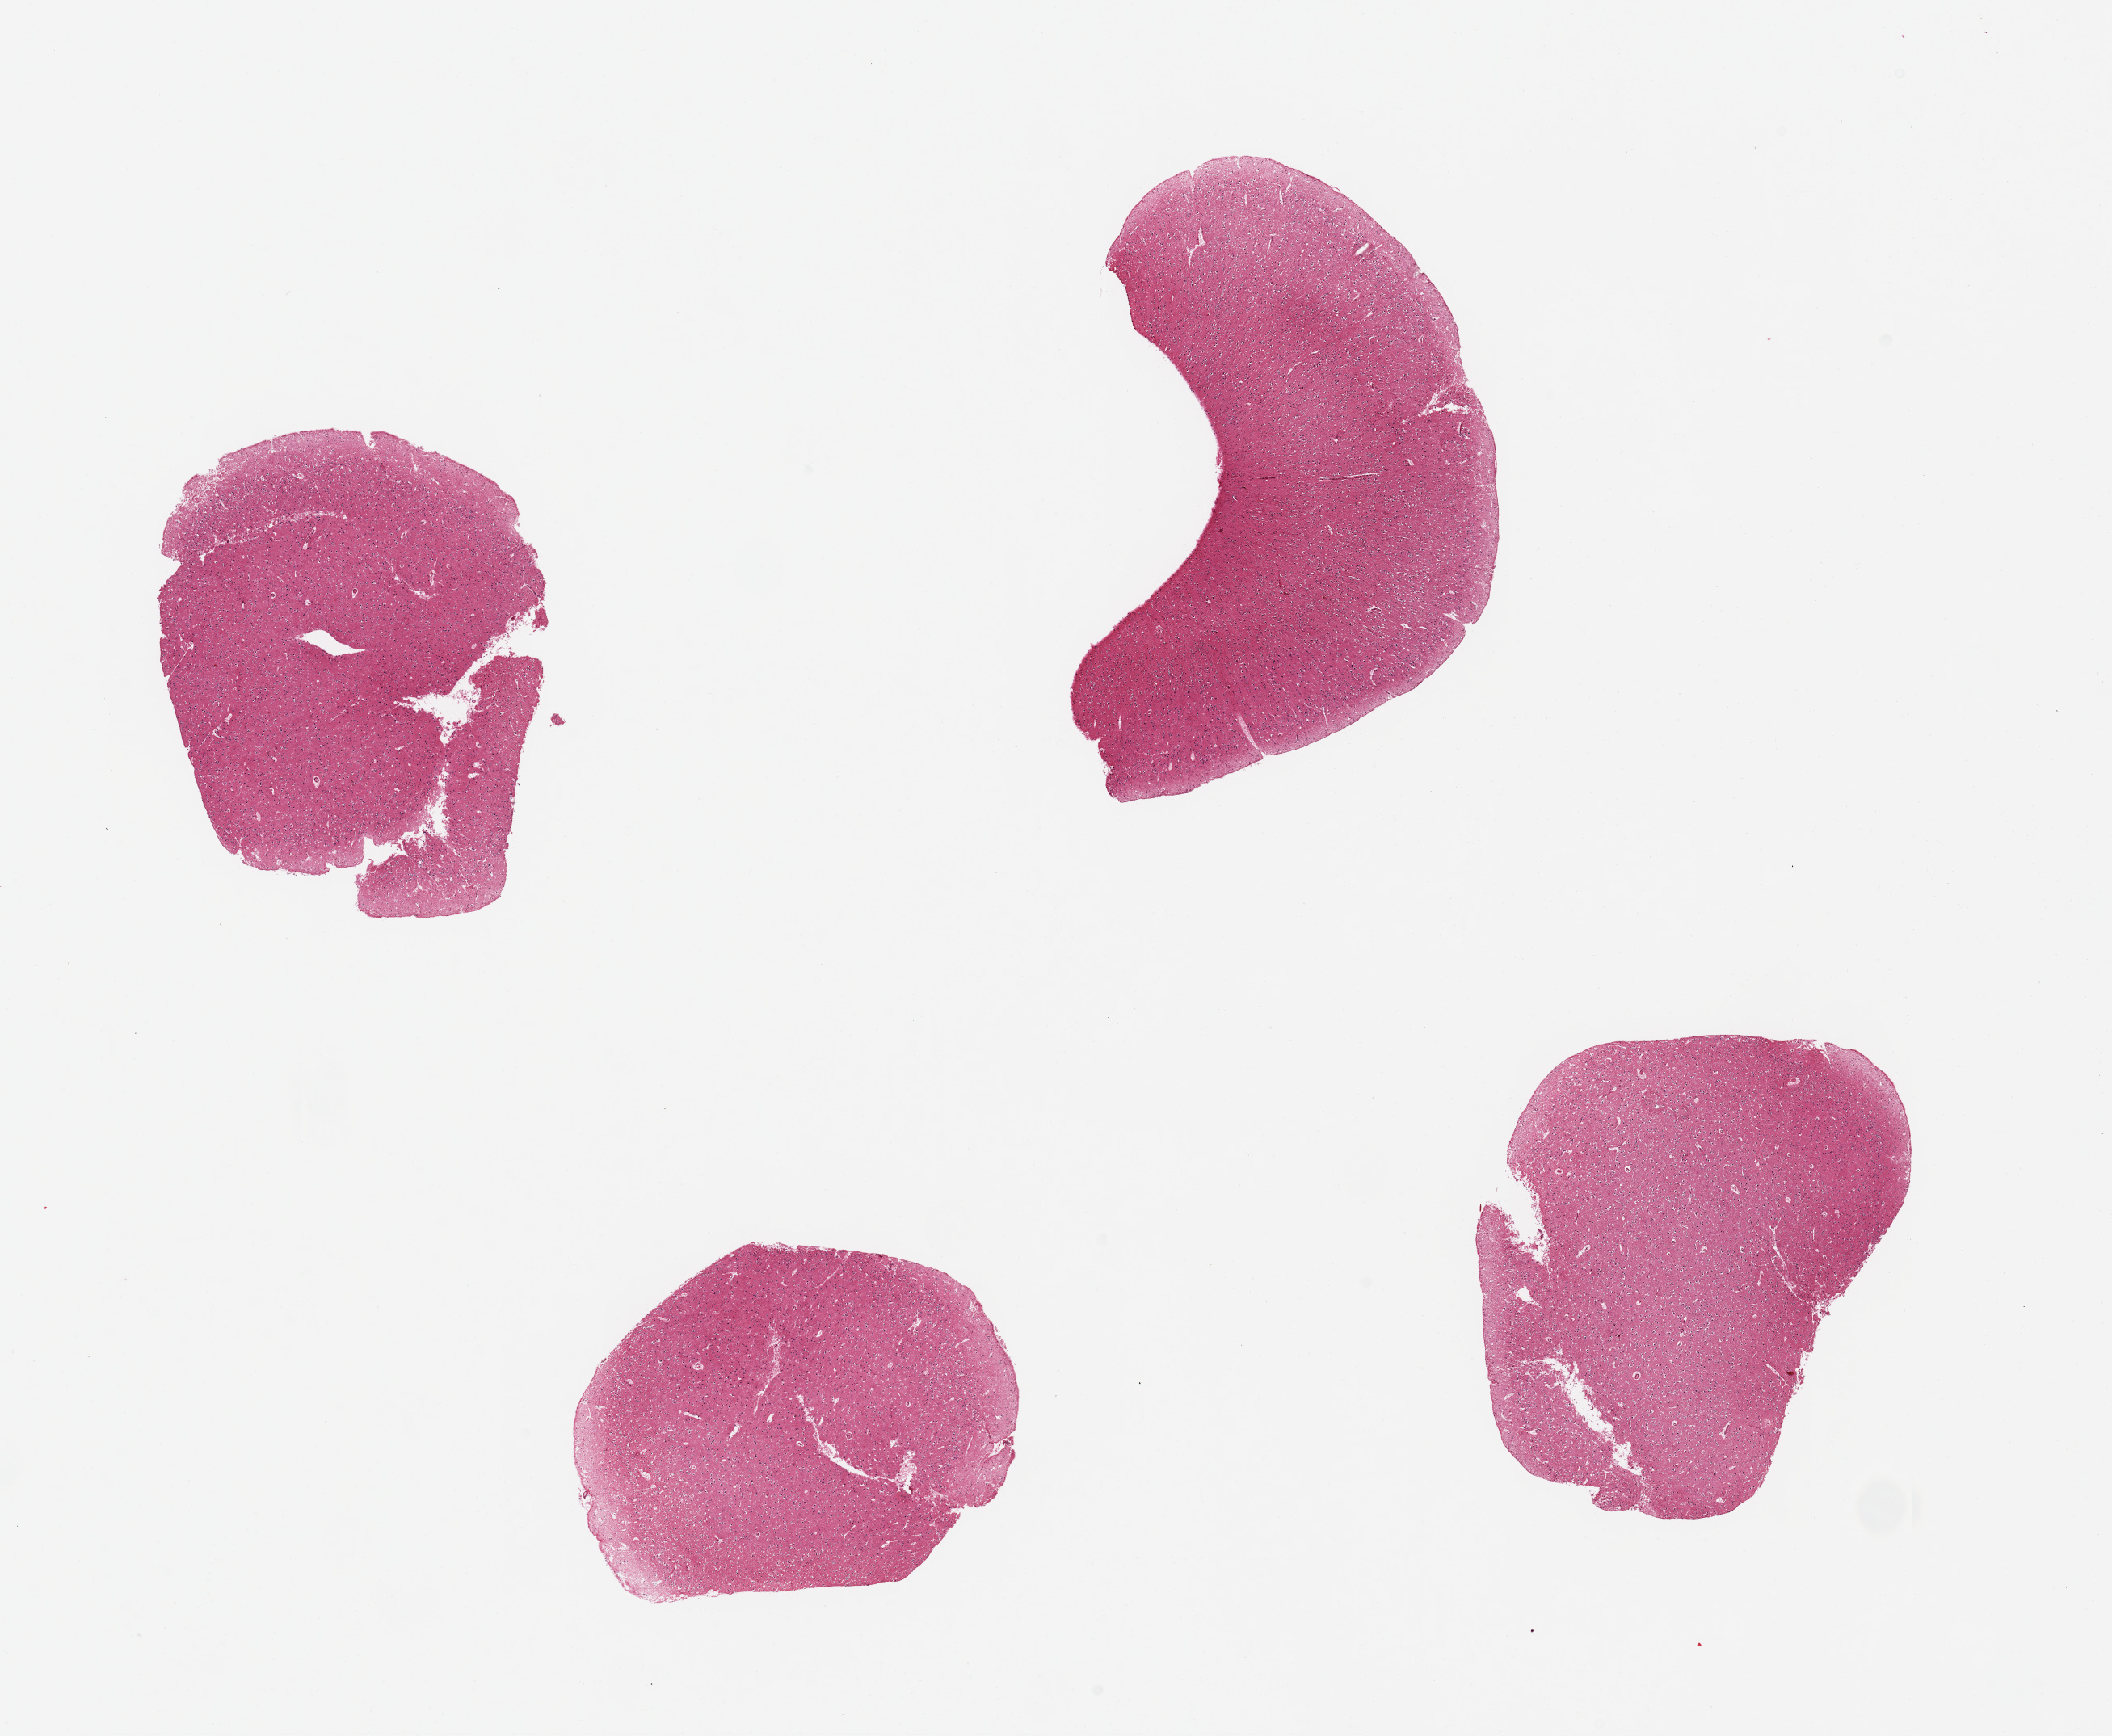
Haematoxylin and eosin whole-slide image, brightfield — low-resolution overview of the scanned area, about 20.7 x 17.0 mm. PAXgene-fixed, paraffin-embedded tissue. Target tissue: cerebral cortex. Donor tissue sample. Donor sex: male.
Review note (as recorded): 4 pieces.